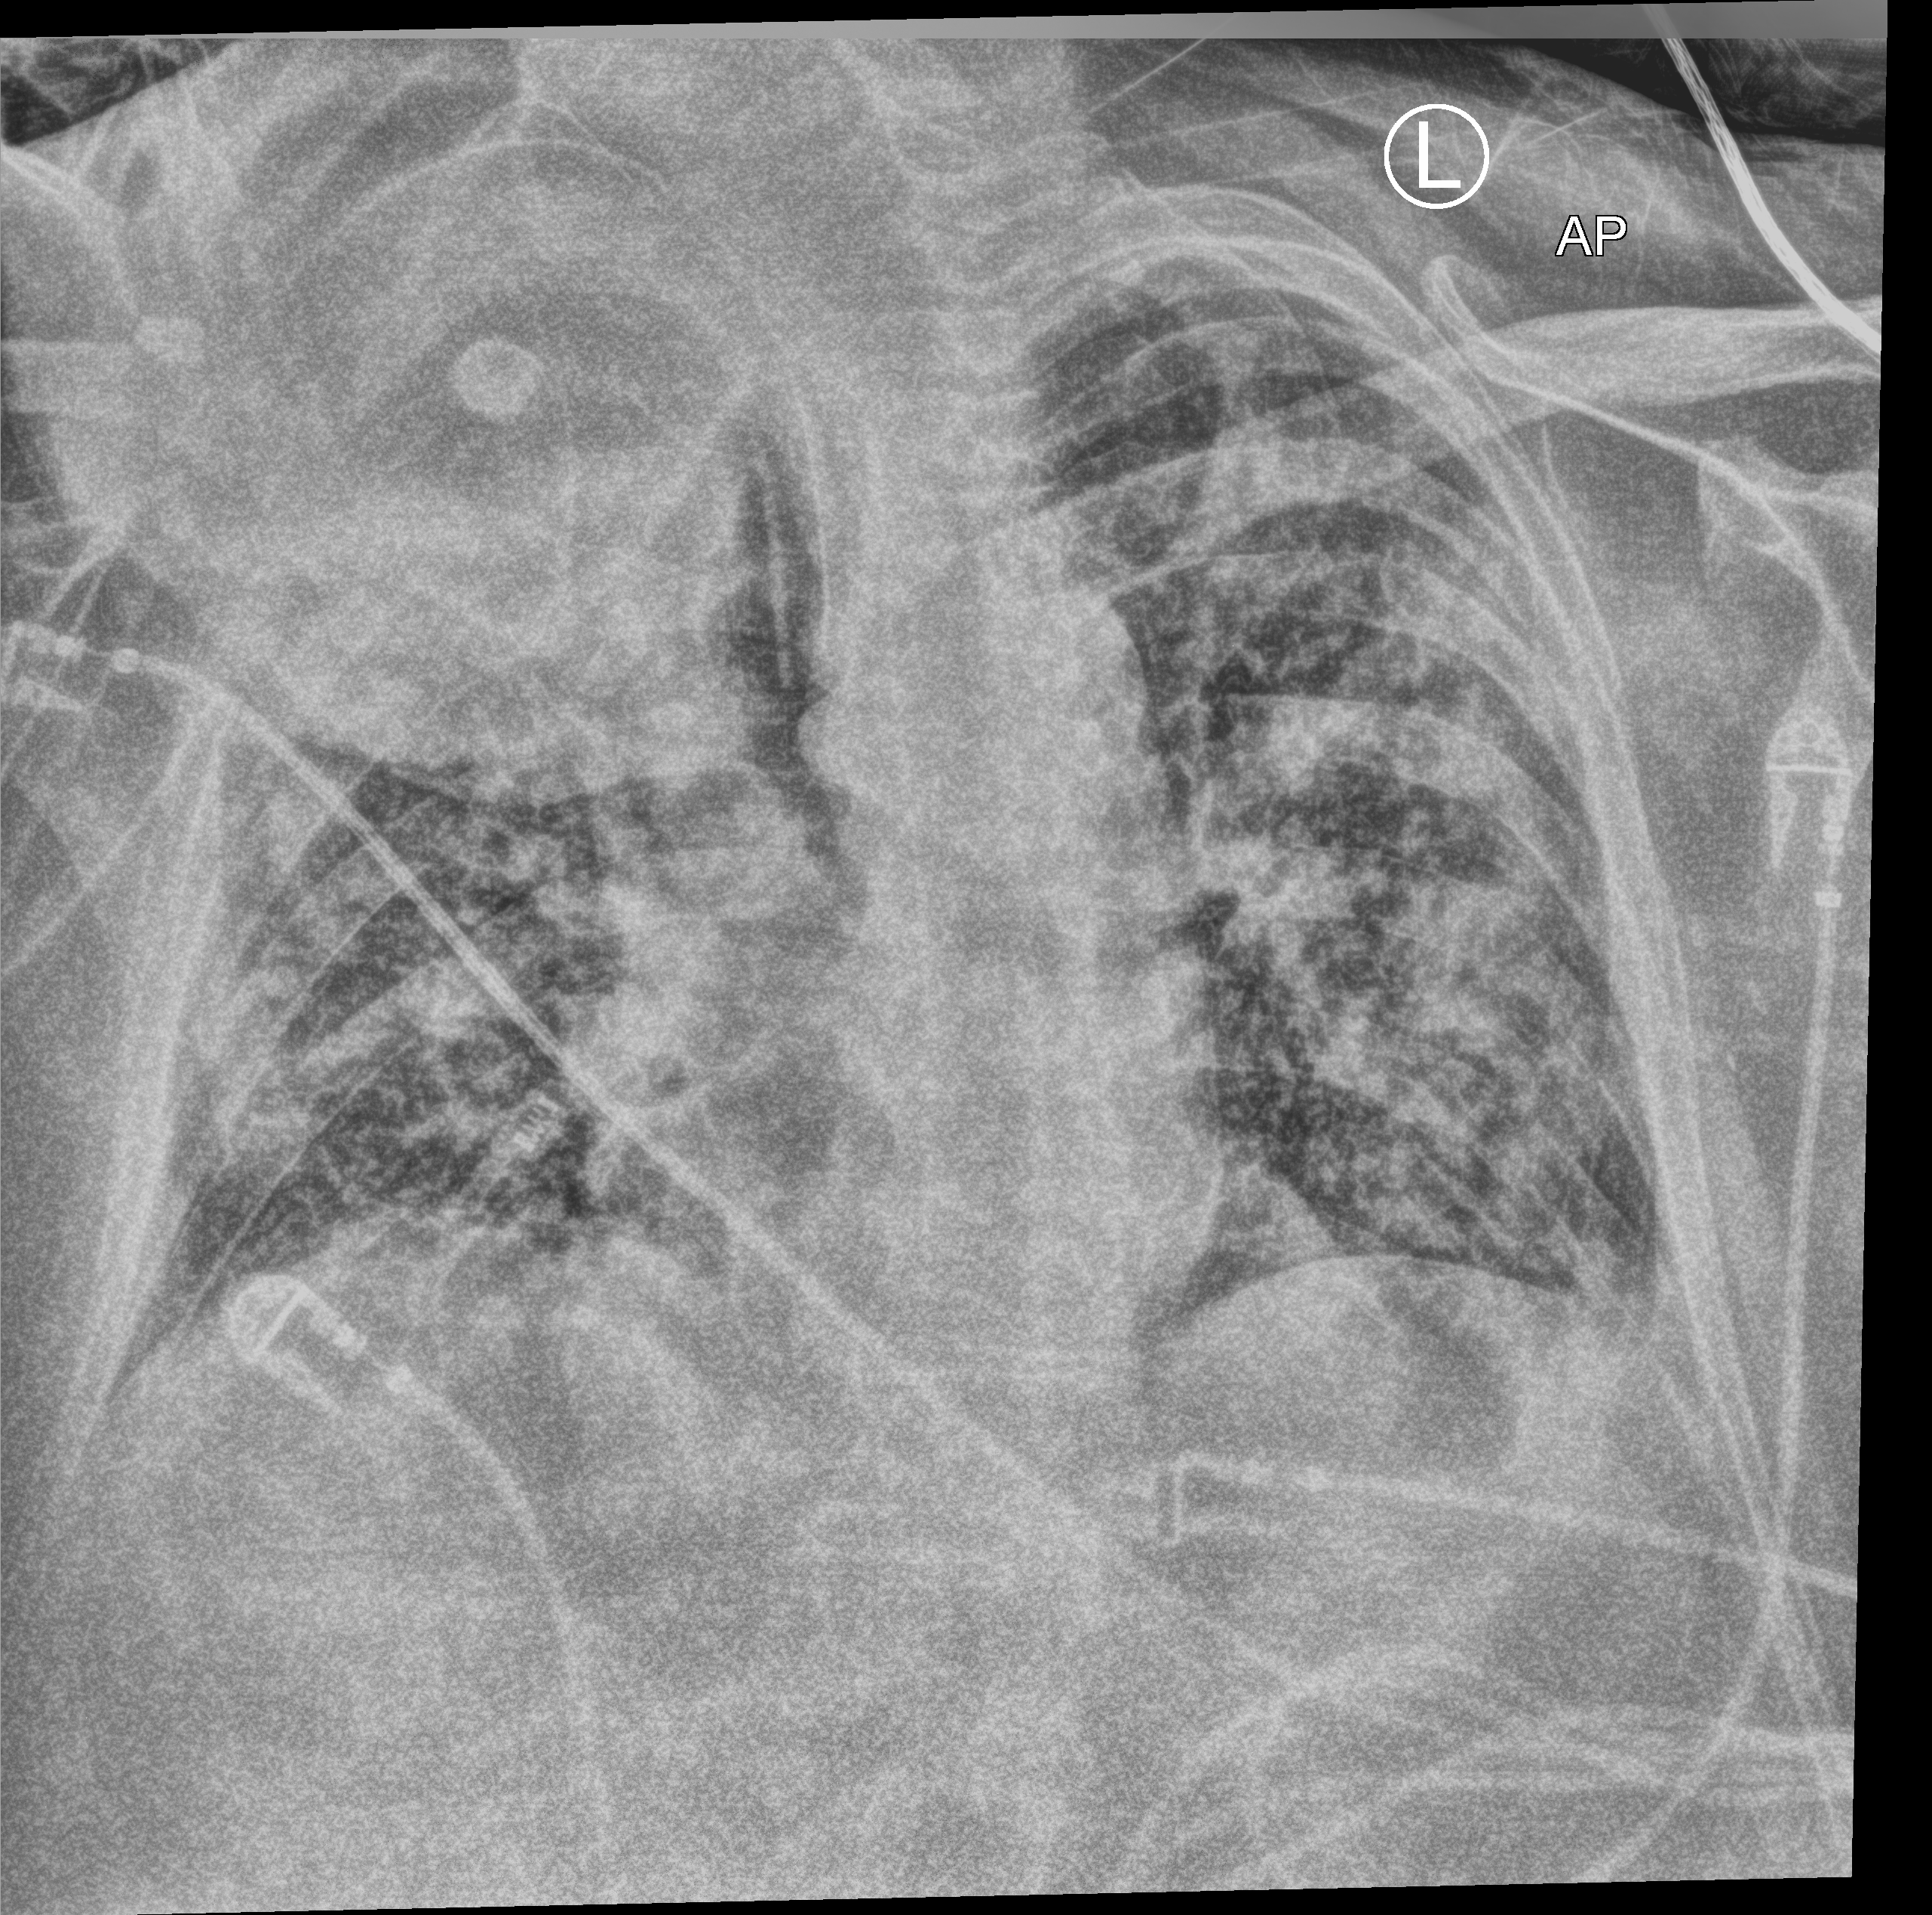
Portable chest radiograph; anteroposterior (AP) projection. Patient hospitalised with COVID-19; male, aged 60–74 years.
From the hospital-stay record, not from the radiograph (when in the stay this image was taken is not recorded):
- other chronic lung disease (admission record): no
- chronic kidney disease (admission record): no
- mechanically ventilated during this hospital stay: yes